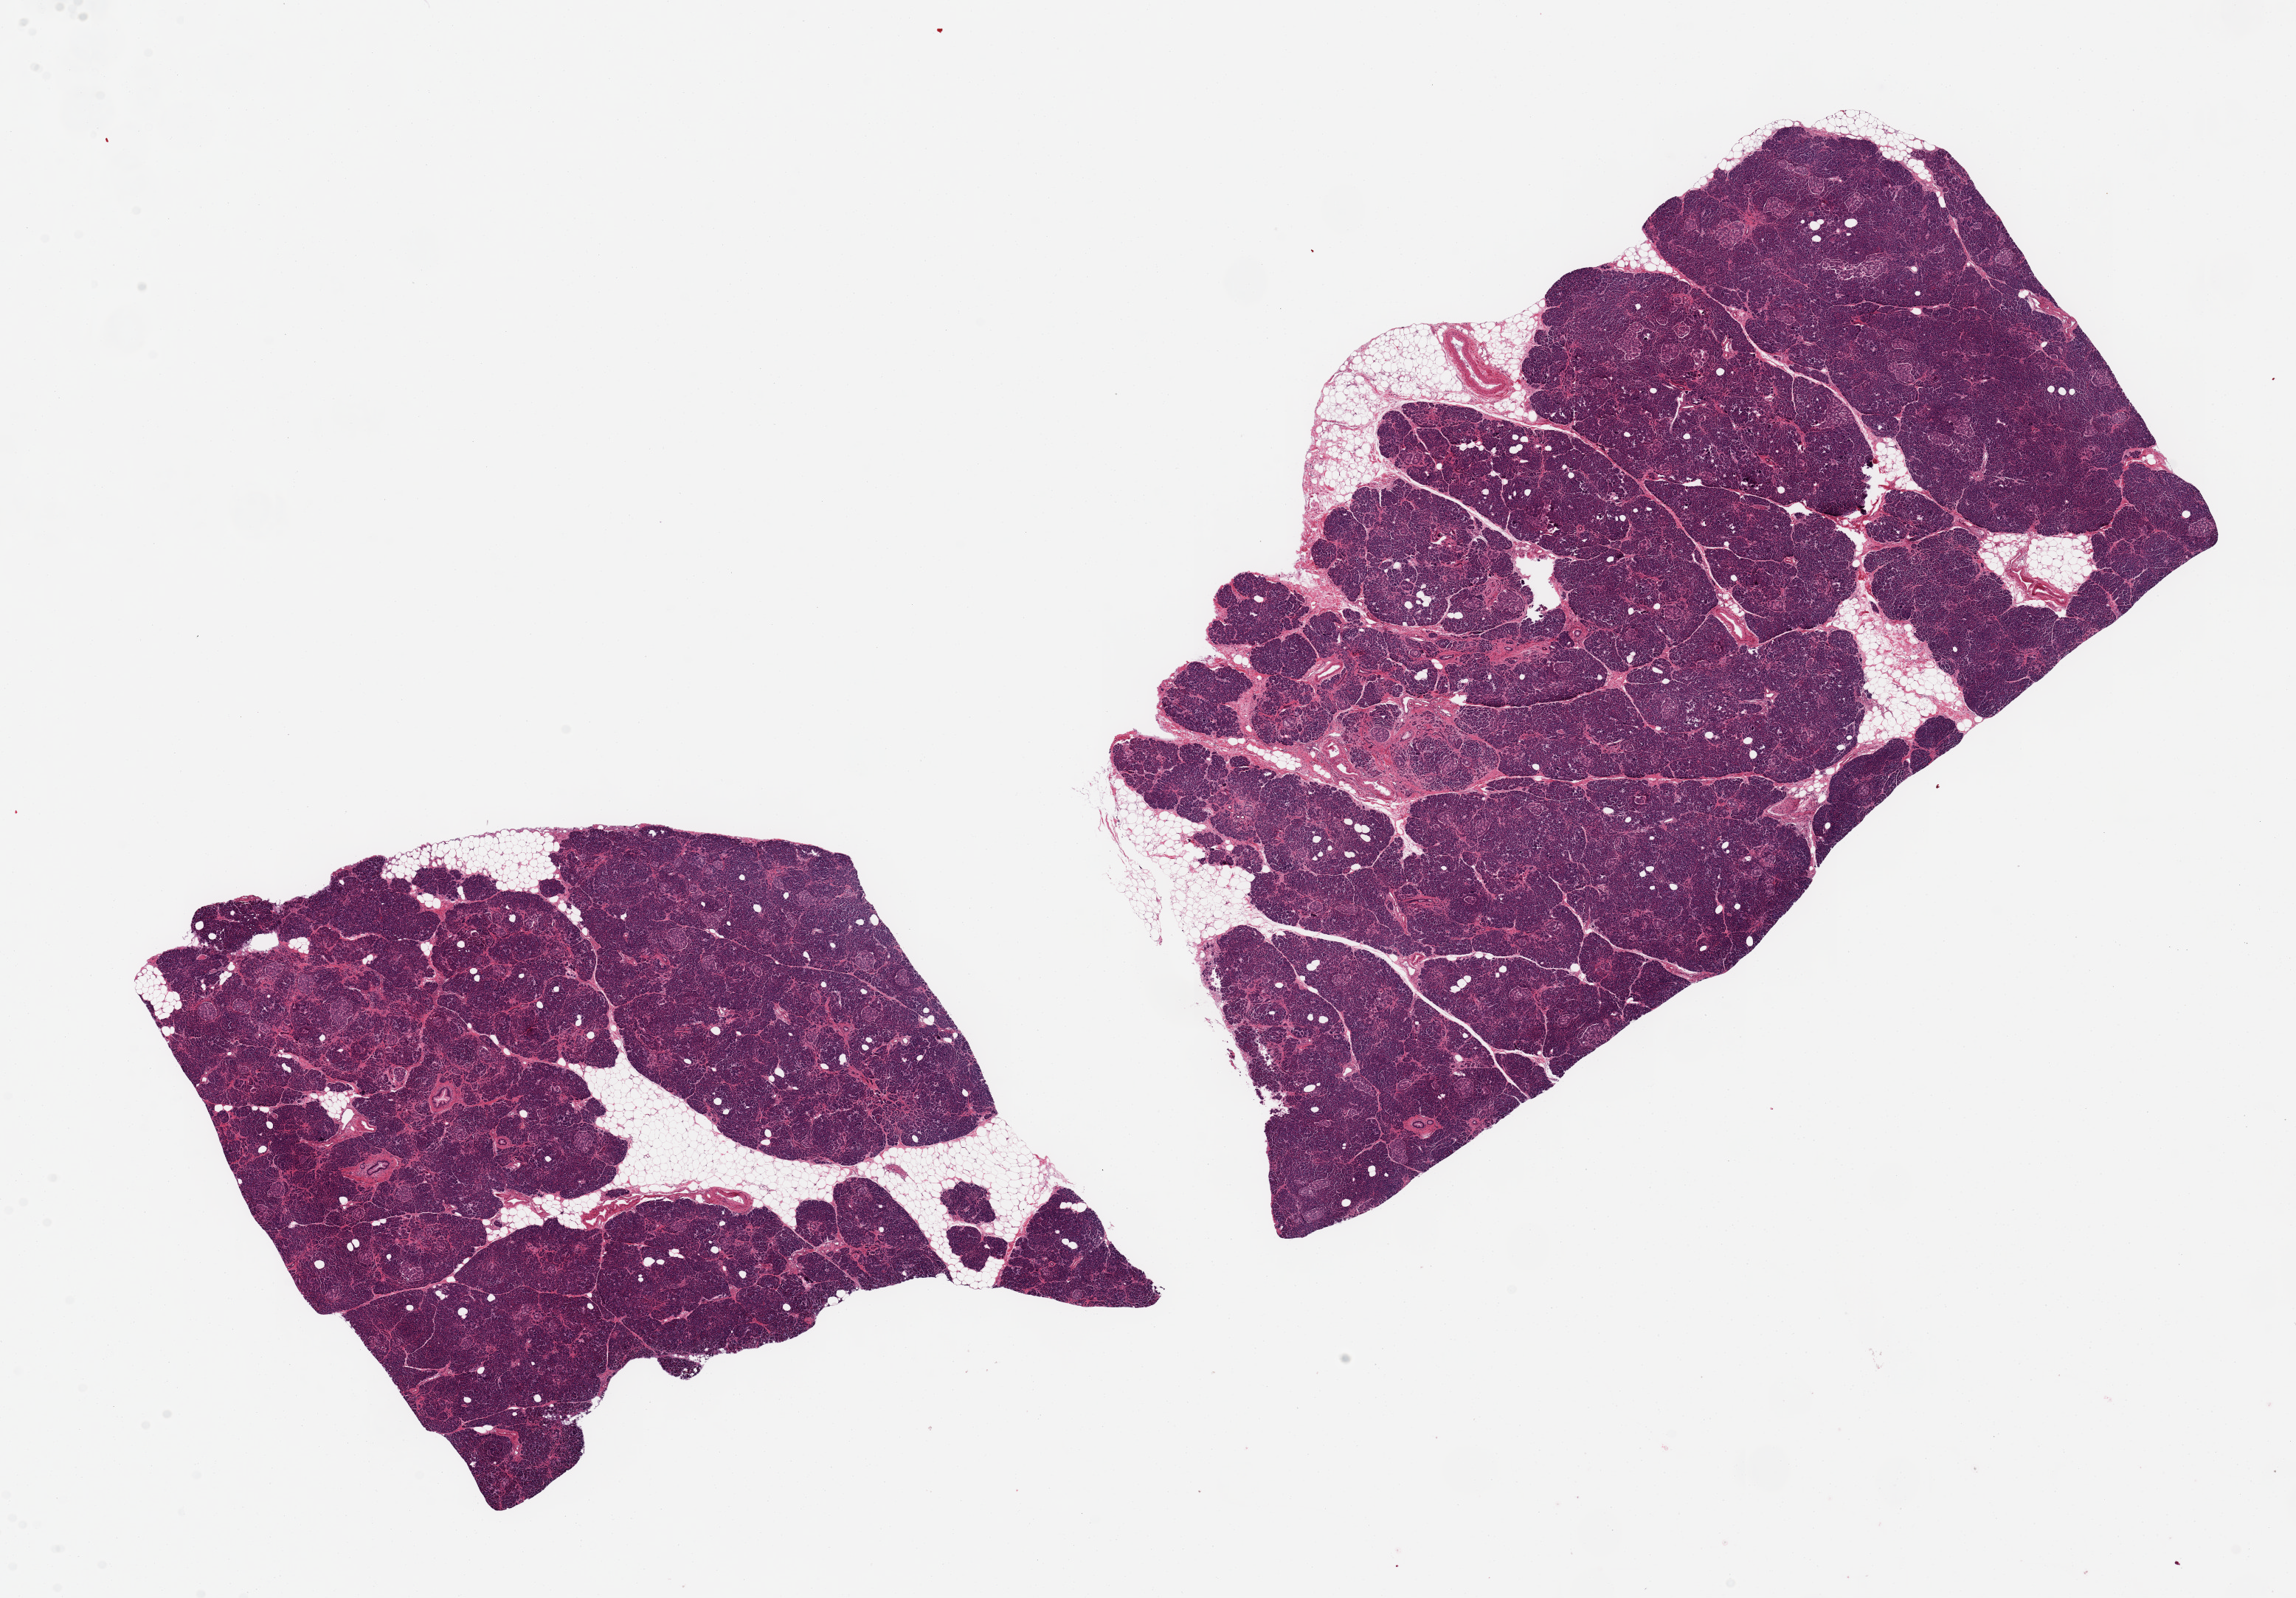
Whole-slide image, hematoxylin and eosin (H&E) stain, brightfield — shown as a low-resolution overview of the whole scanned area (about 24.6 x 17.1 mm). PAXgene-fixed, paraffin-embedded tissue. Section of pancreas (target tissue). Donor tissue sample. Donor sex: female.
* review note (as recorded): 2 ~ 9x7mm pieces, remarkably well-preserved; good clean specimens. Minimal peri-pancreatic saponification